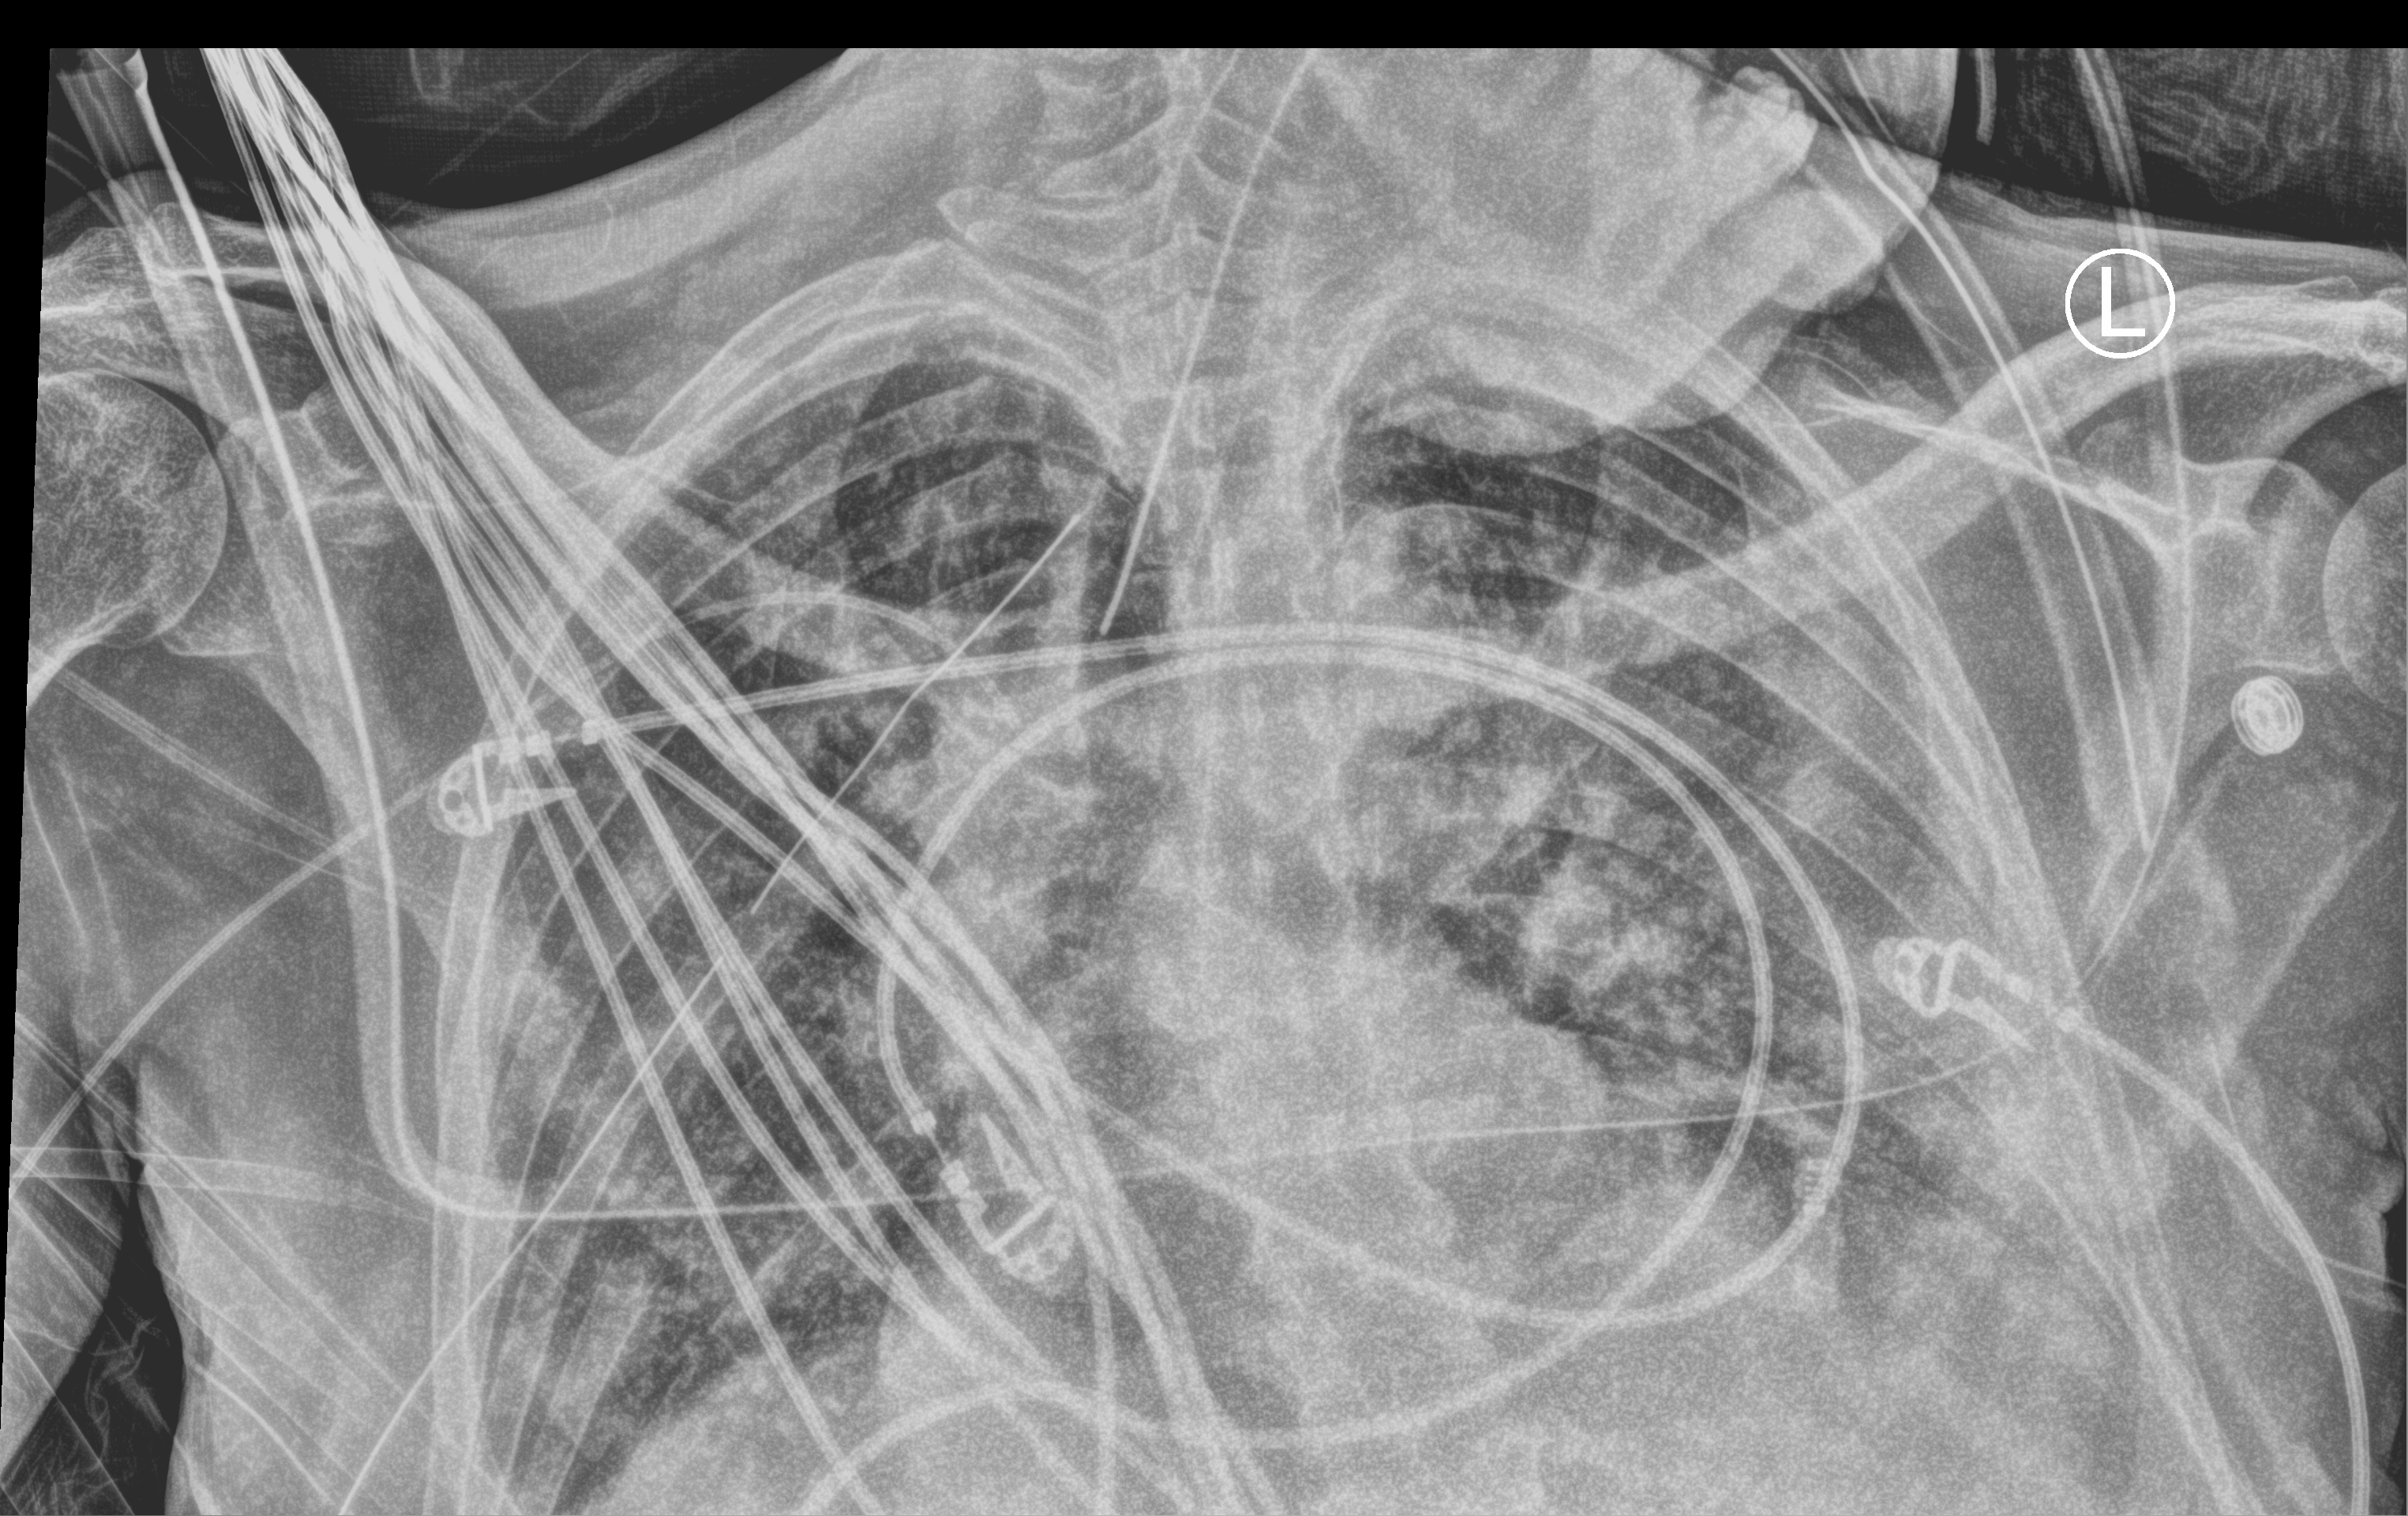
Bedside chest radiograph (computed radiography), anteroposterior (AP) projection. Male patient hospitalised with COVID-19, age 18–59 years.
Hospital-stay facts (about this admission, not read from this image; timing relative to this image not recorded):
- mechanically ventilated during this hospital stay: yes
- admitted to intensive care during this hospital stay: yes